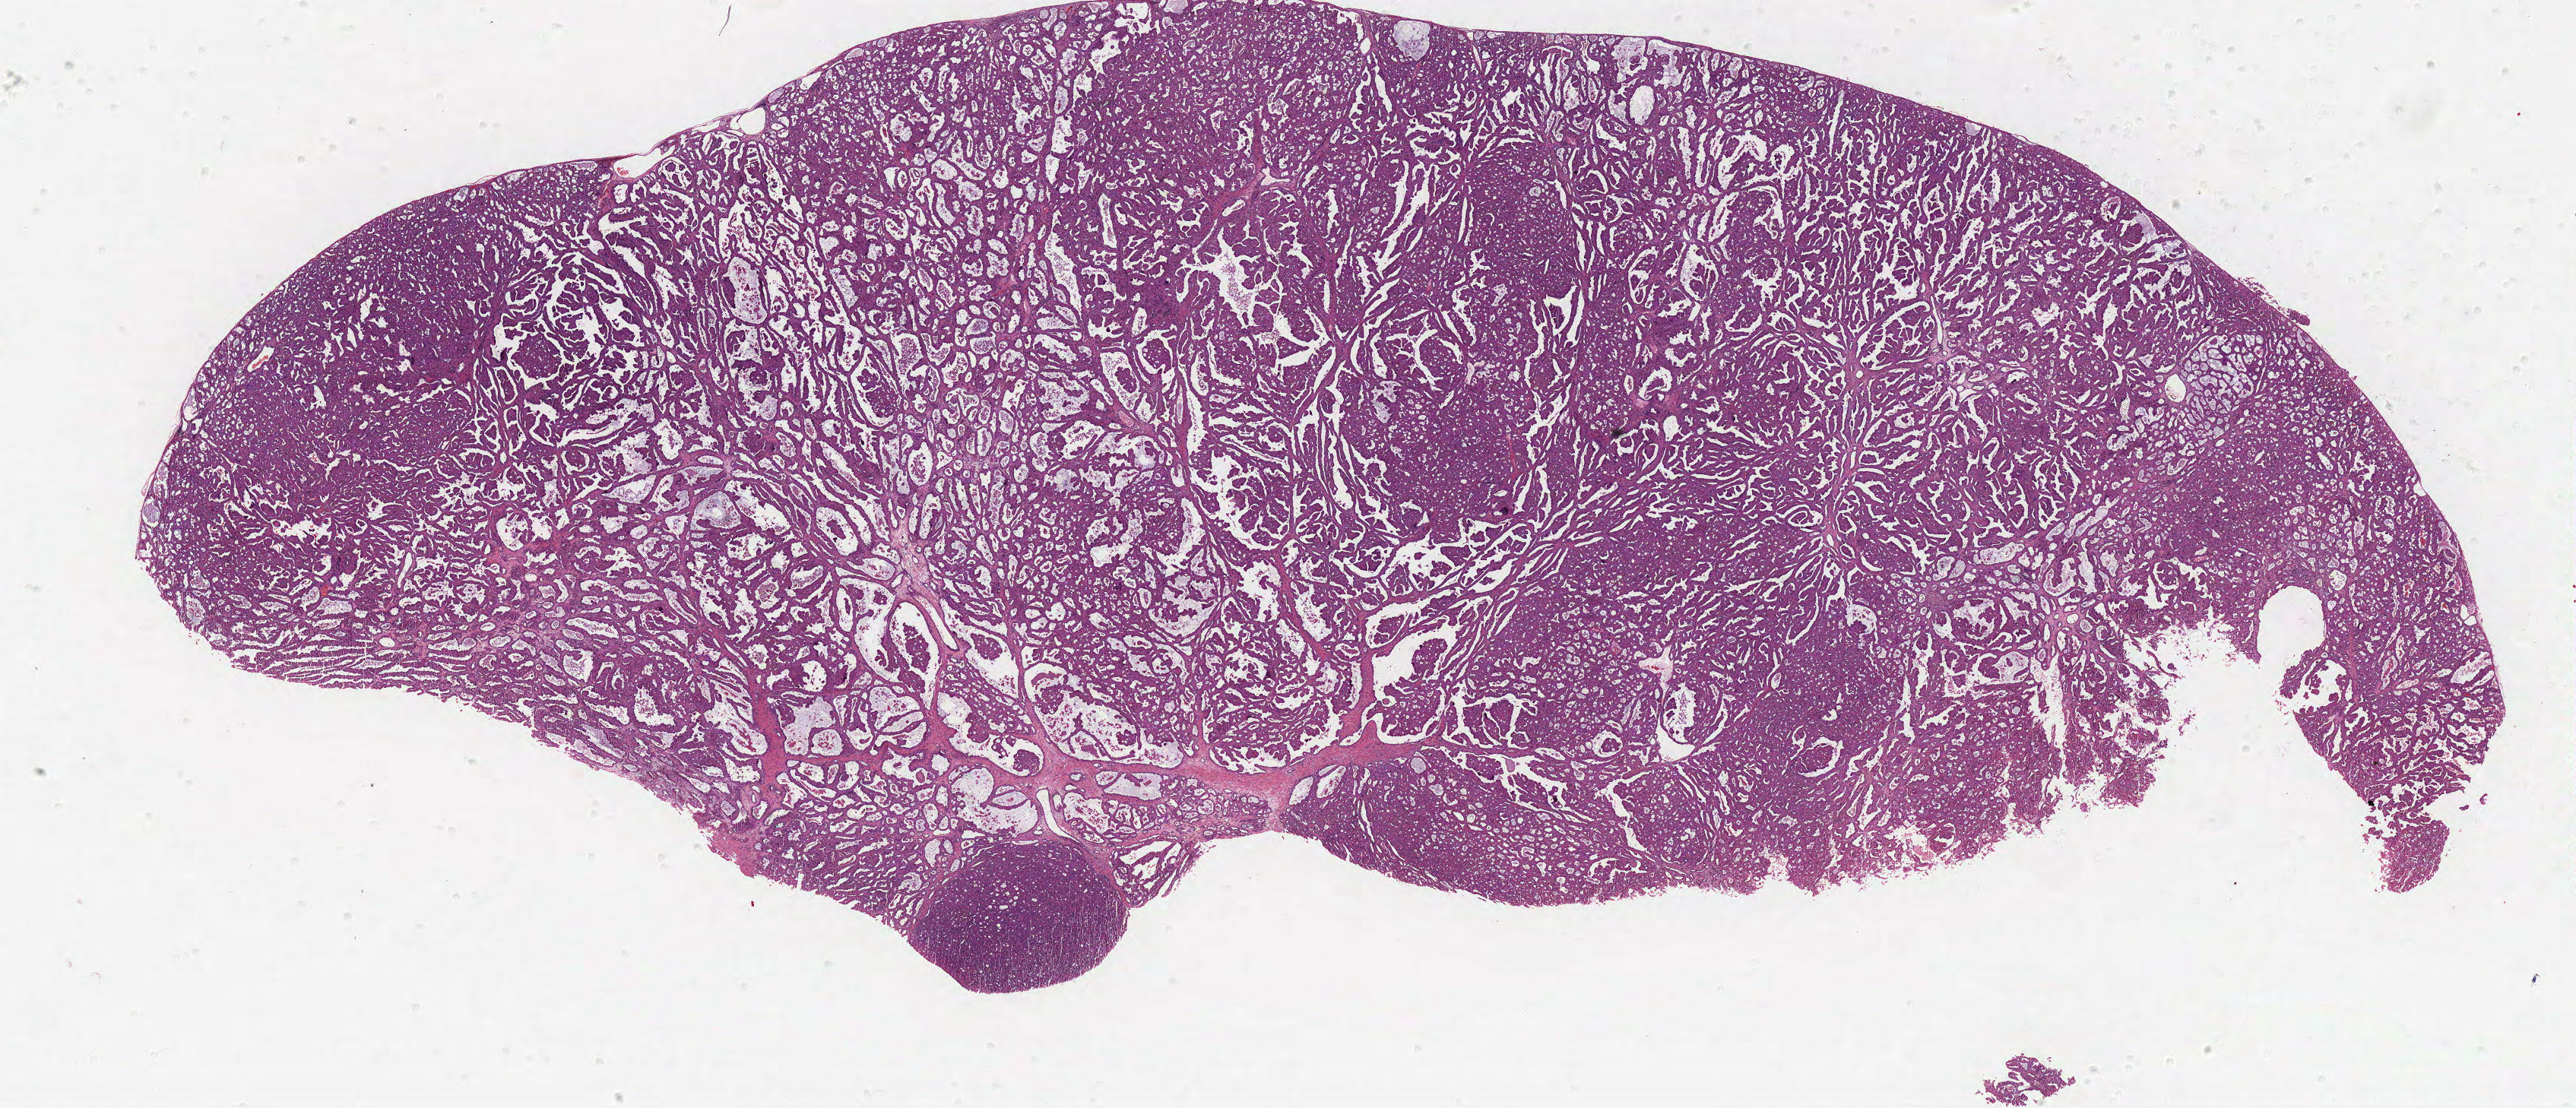
Digitized H&E tissue section (whole slide) — low-resolution overview of the scanned area, about 27.1 x 11.7 mm (slide scanned at 40x); formalin-fixed paraffin-embedded (FFPE) diagnostic section; kidney, primary tumour sample. Patient: female, age at initial diagnosis 79 years.
Histologic diagnosis: Papillary adenocarcinoma, NOS. Laterality: right. AJCC pathologic stage: I (6th edition).